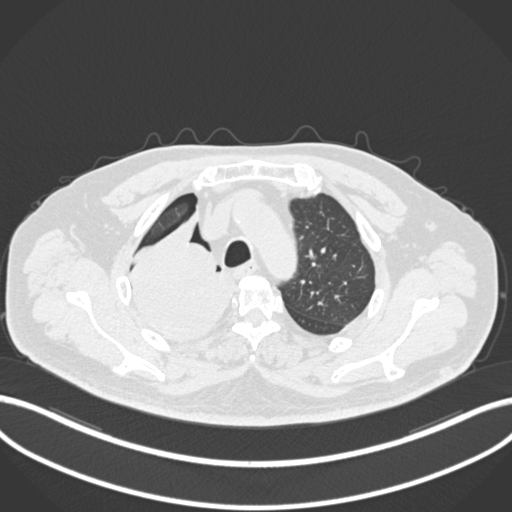
Chest CT, one axial slice. Slice 166 of 218 in the series (ordered by position). Reconstruction kernel B30f. Lung window (W 1500 / L -600 HU). 1 mm slice thickness. 512 × 512 image matrix, field of view 400 × 400 mm. Male patient, age 68 years. Case-level facts recorded for this patient, not image findings: clinical TNM (as recorded): T2a N0 M0.
Outlined on this slice (rectangle marked by the reading radiologist):
- lung tumour (recorded histology: adenocarcinoma): bounding box <131,233,232,350> (left, top, right, bottom; pixels)